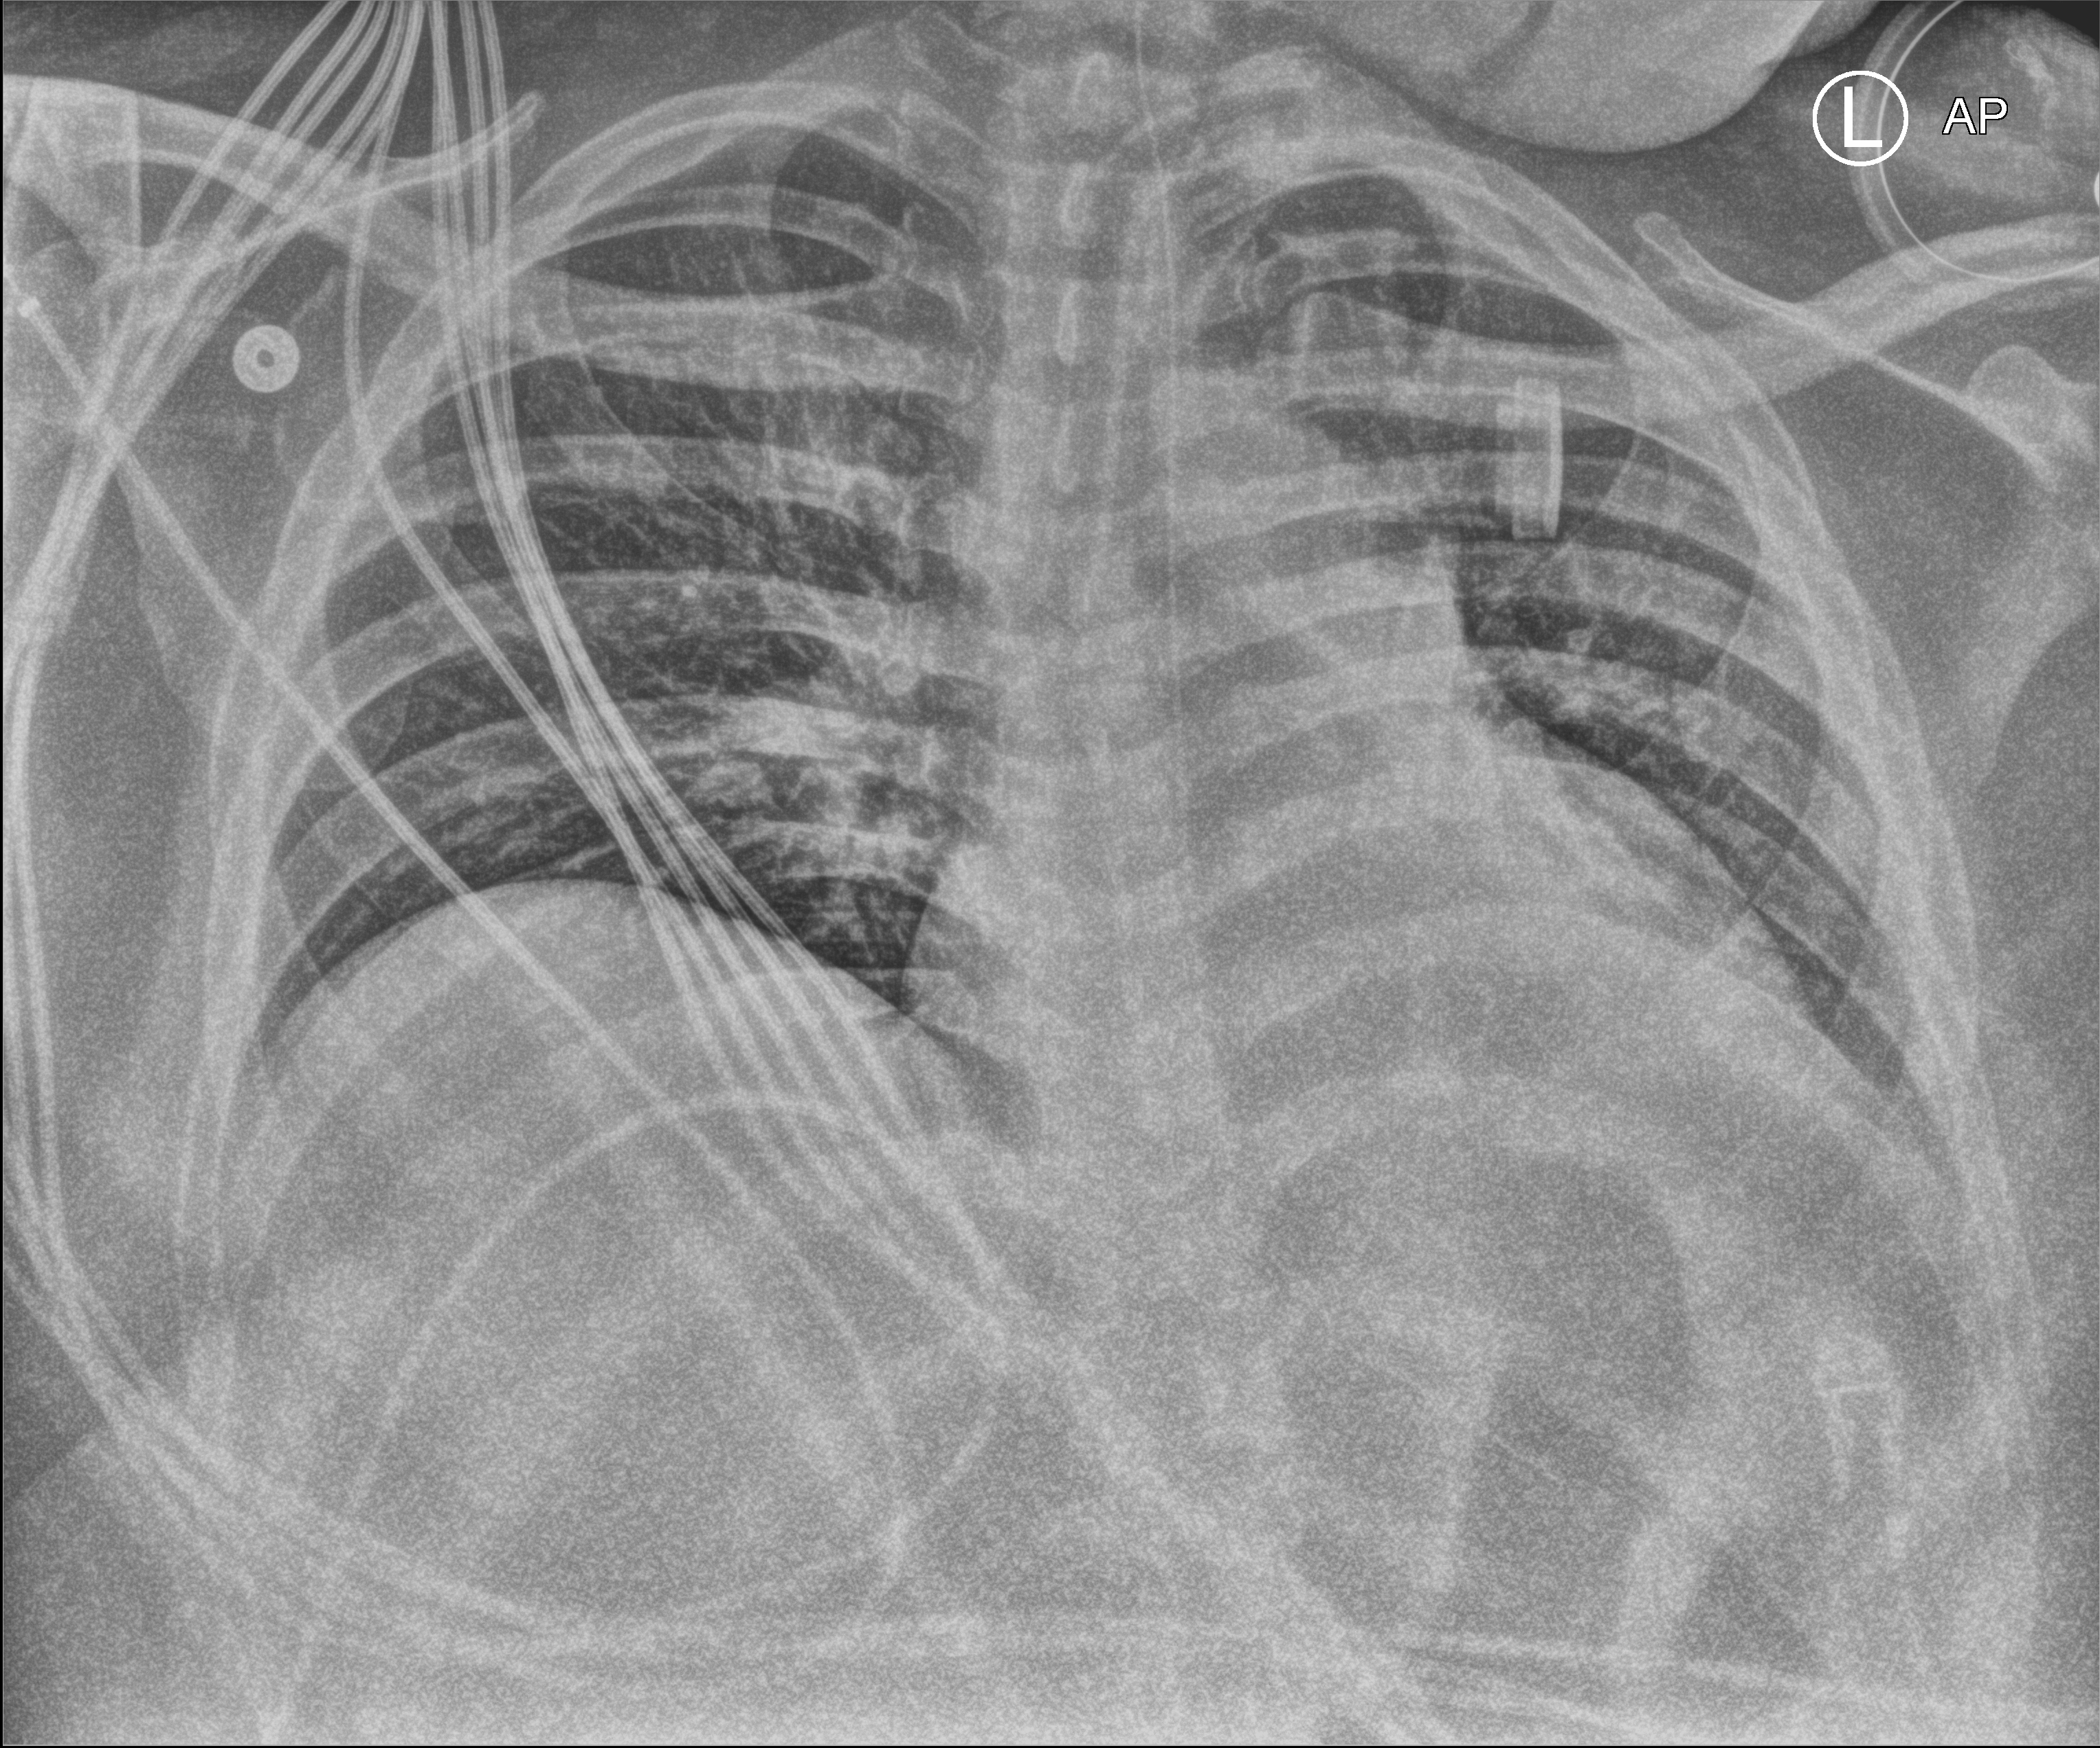
Bedside chest radiograph (computed radiography); anteroposterior (AP) projection. Male patient hospitalised with COVID-19, age 18–59 years.
From the hospital-stay record, not from the radiograph (when in the stay this image was taken is not recorded):
- hypertension (admission record): no